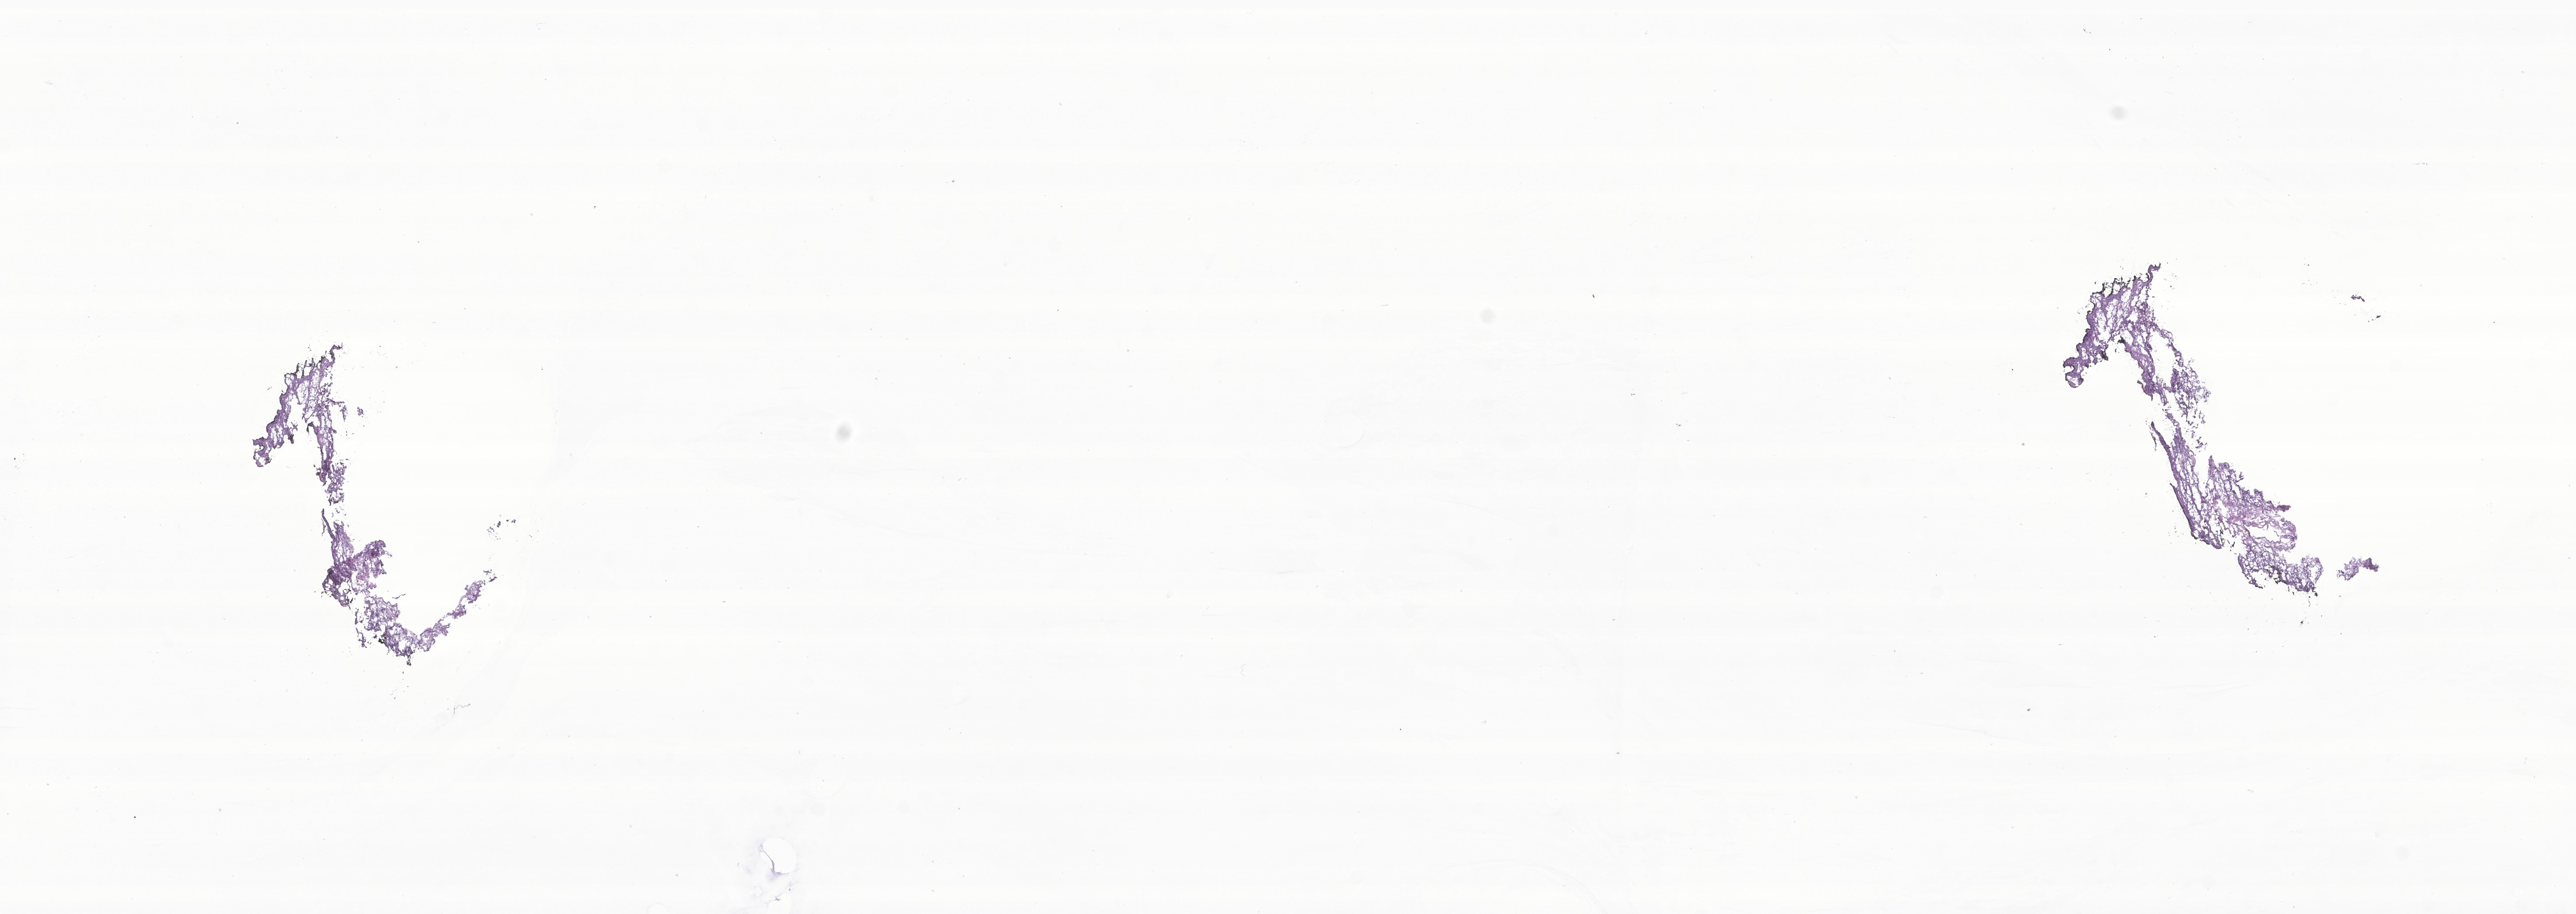
Whole-slide image, hematoxylin and eosin (H&E) stain of tumor tissue from the orbit — shown as a low-resolution overview of the whole scanned area (about 18.6 x 6.6 mm). Cryosection (OCT / tissue freezing medium). Patient female; age 60 months (5 years).
- diagnosis (ICD-O-3 morphology term): Embryonal rhabdomyosarcoma, NOS